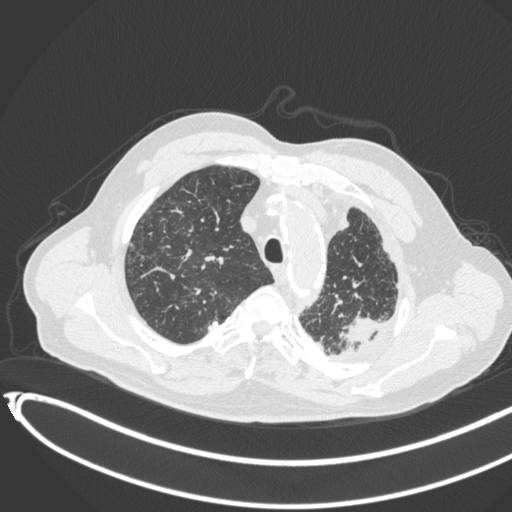
Chest CT, one axial slice. Position 342 of 451 along the scan axis. Lung window (W 1500 / L -600 HU). 1 mm slice thickness. 512 × 512 image matrix, field of view 400 × 400 mm. Patient: male, 78 years. Case-level facts recorded for this patient, not image findings: clinical TNM (as recorded): T1c N0 M1.
Annotated regions visible in this slice (rectangle marked by the reading radiologist):
- lung tumour (recorded histology: adenocarcinoma): box from (x=334, y=313) to (x=384, y=346) px